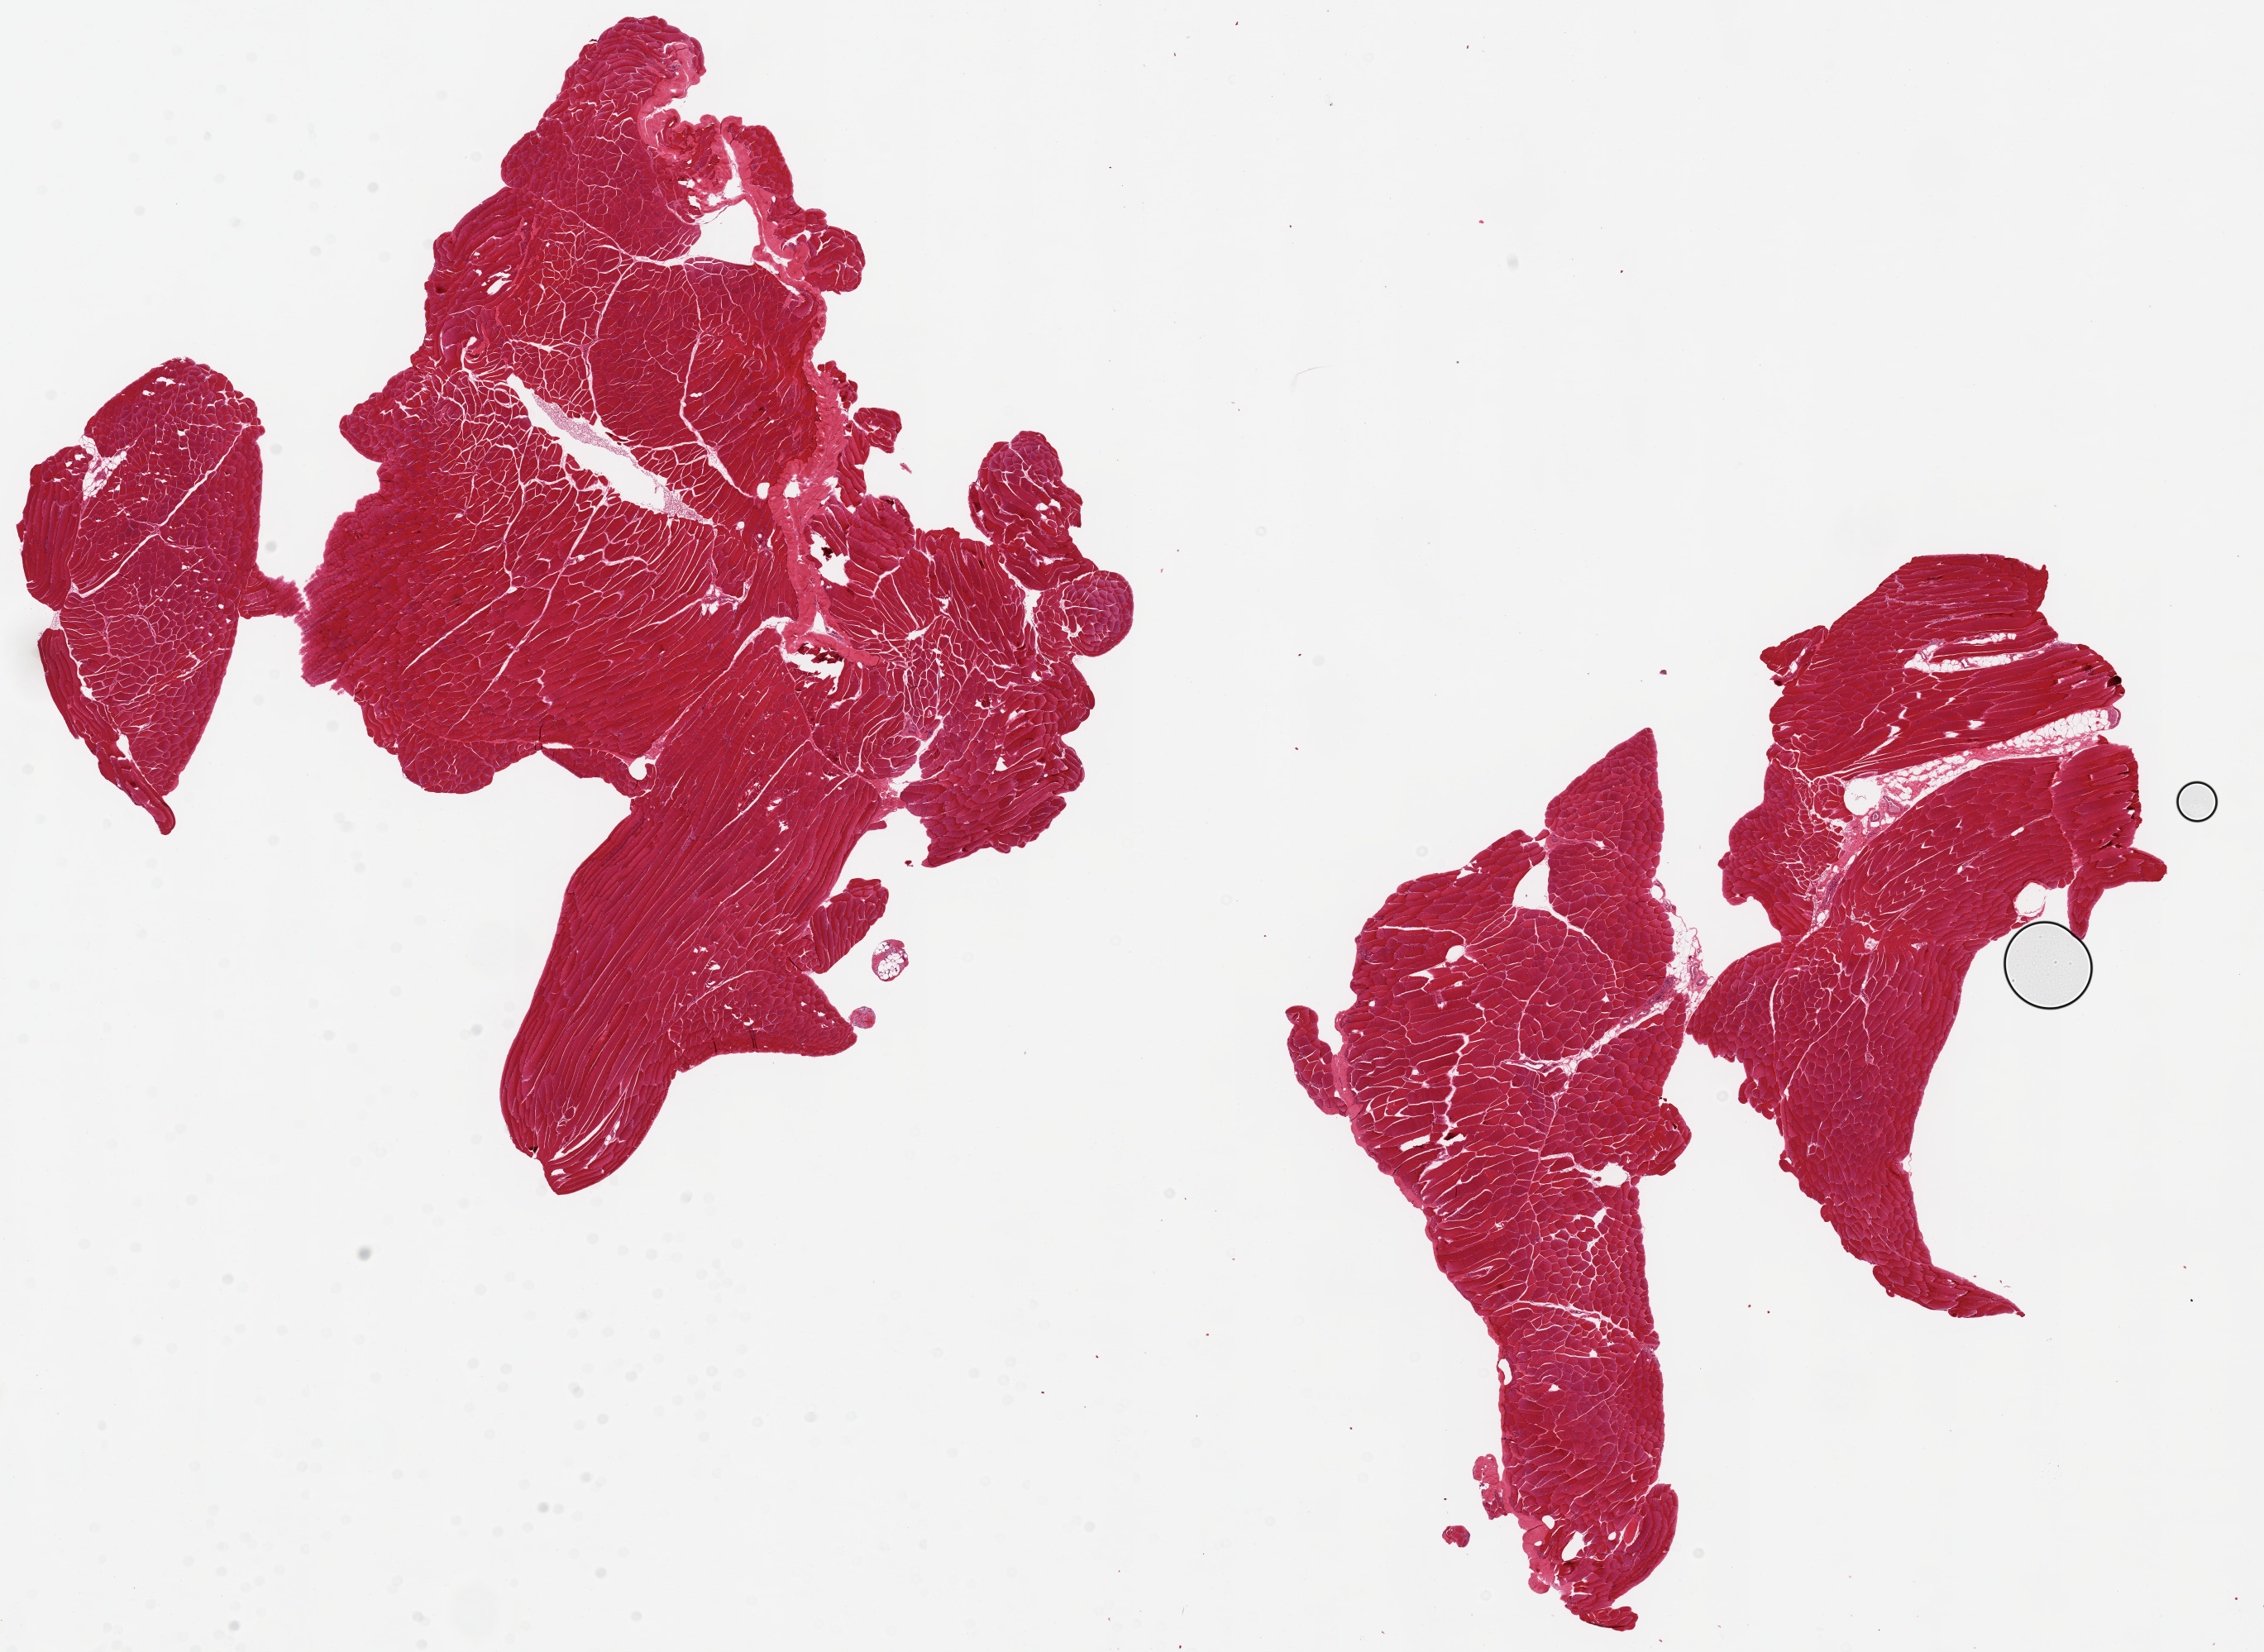
H&E whole-slide image — whole scanned area (about 21.7 x 15.8 mm) shown as a low-resolution overview; PAXgene-fixed paraffin-embedded (PFPE) section; sampled site (target tissue): skeletal muscle; tissue donor sample.
Reviewer comment on this tissue sample: 2 pieces ~8x8mm, only trace interstitial fat.